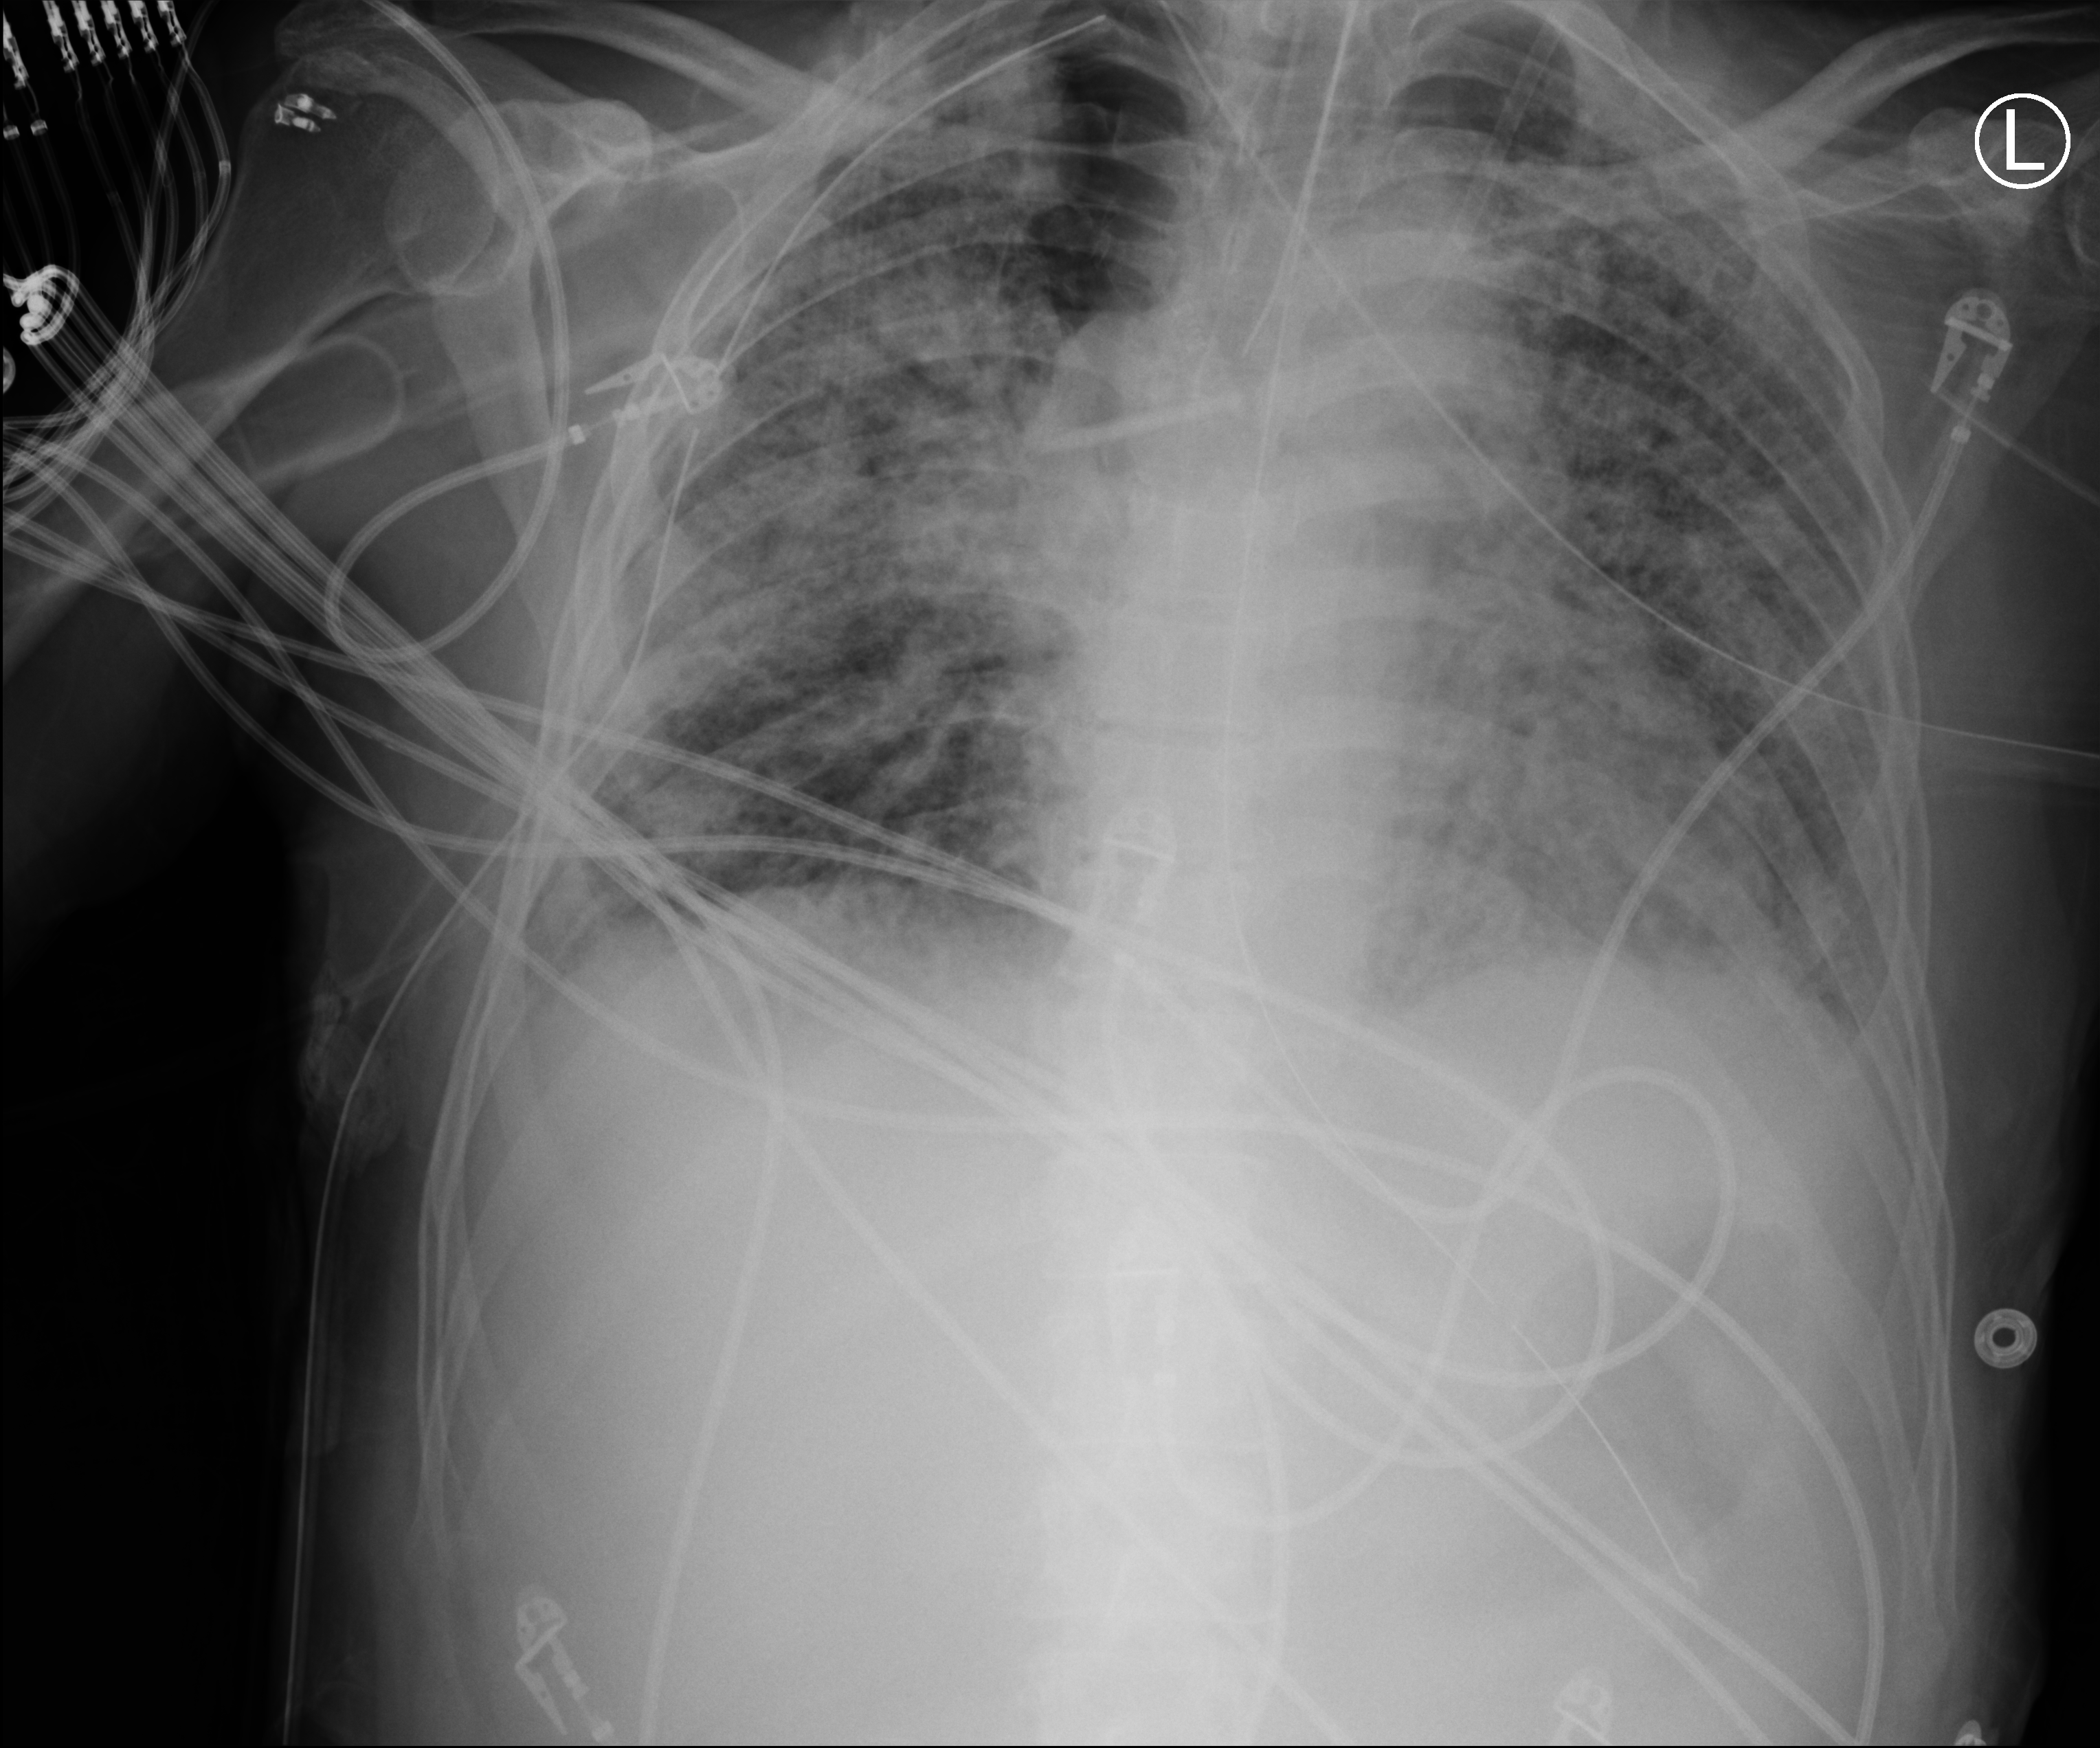
Bedside chest radiograph (computed radiography), anteroposterior (AP) projection. Patient hospitalised with COVID-19; male, aged 60–74 years.
From the hospital-stay record, not from the radiograph (when in the stay this image was taken is not recorded): admitted to intensive care during this hospital stay: yes; diabetes (admission record): no.